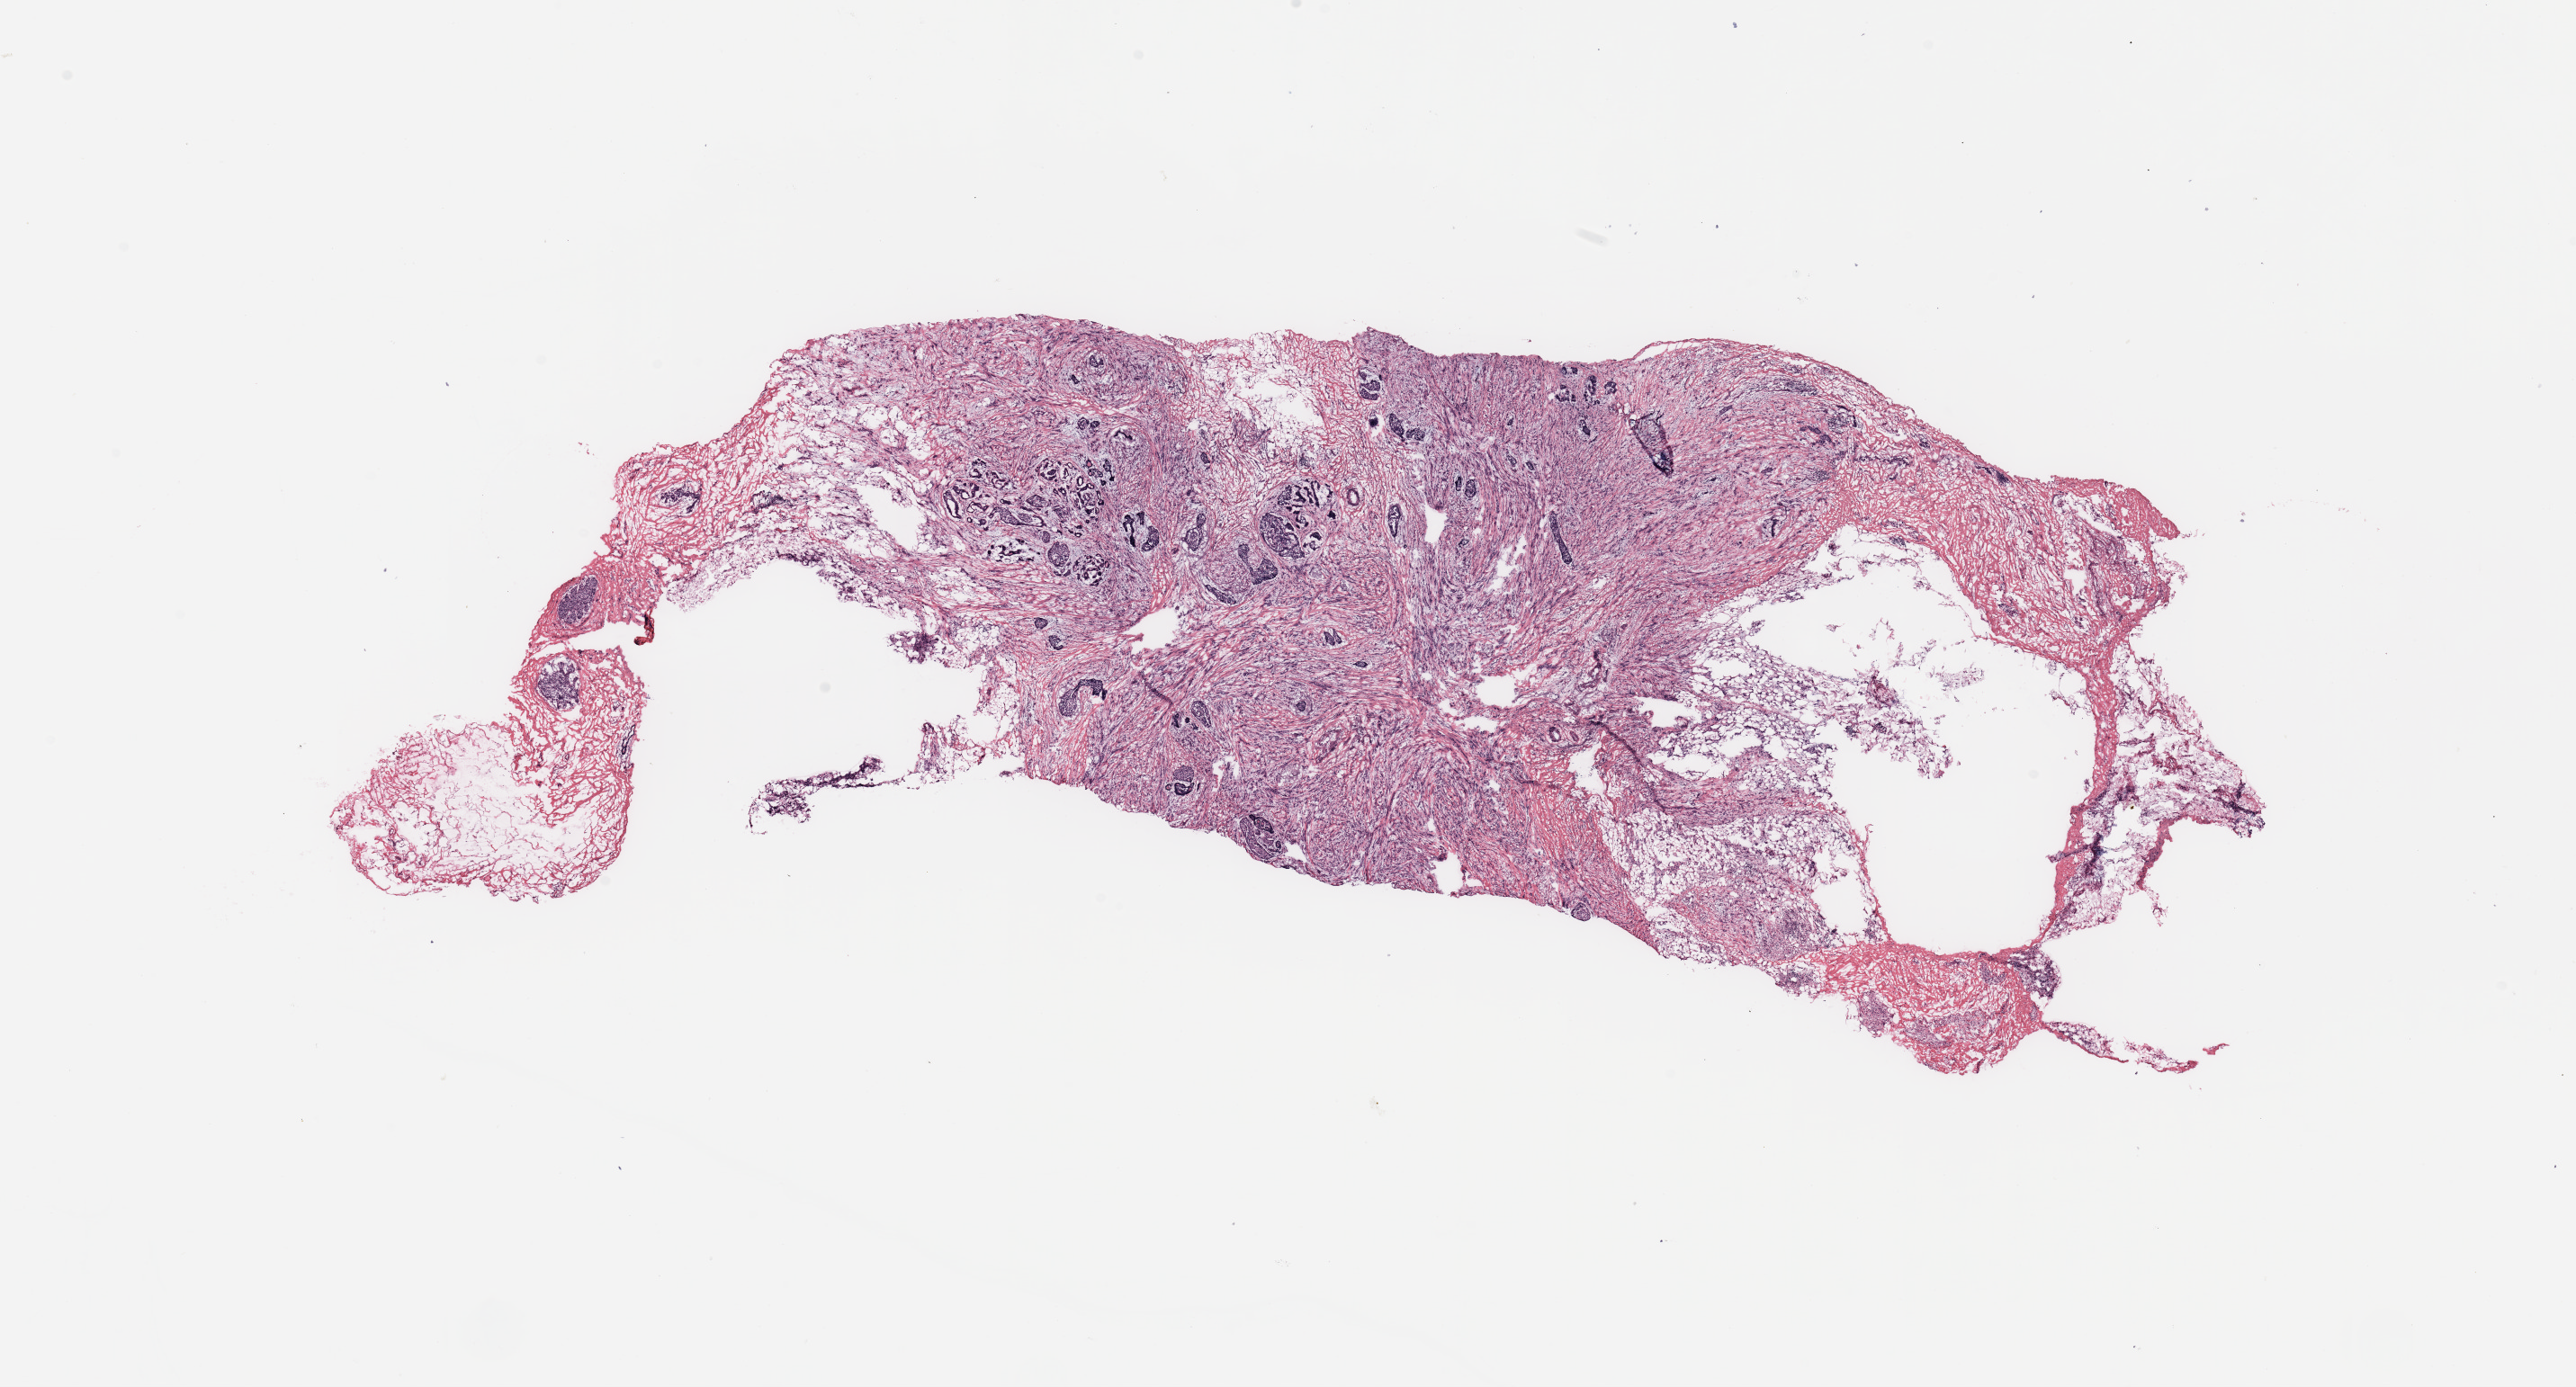
H&E-stained whole-slide image — a low-resolution overview of the entire scanned area, about 22.6 x 12.2 mm (slide scanned at 20x), breast, tissue type not recorded.
Patient diagnosis (cohort enrolment): breast cancer (breast).